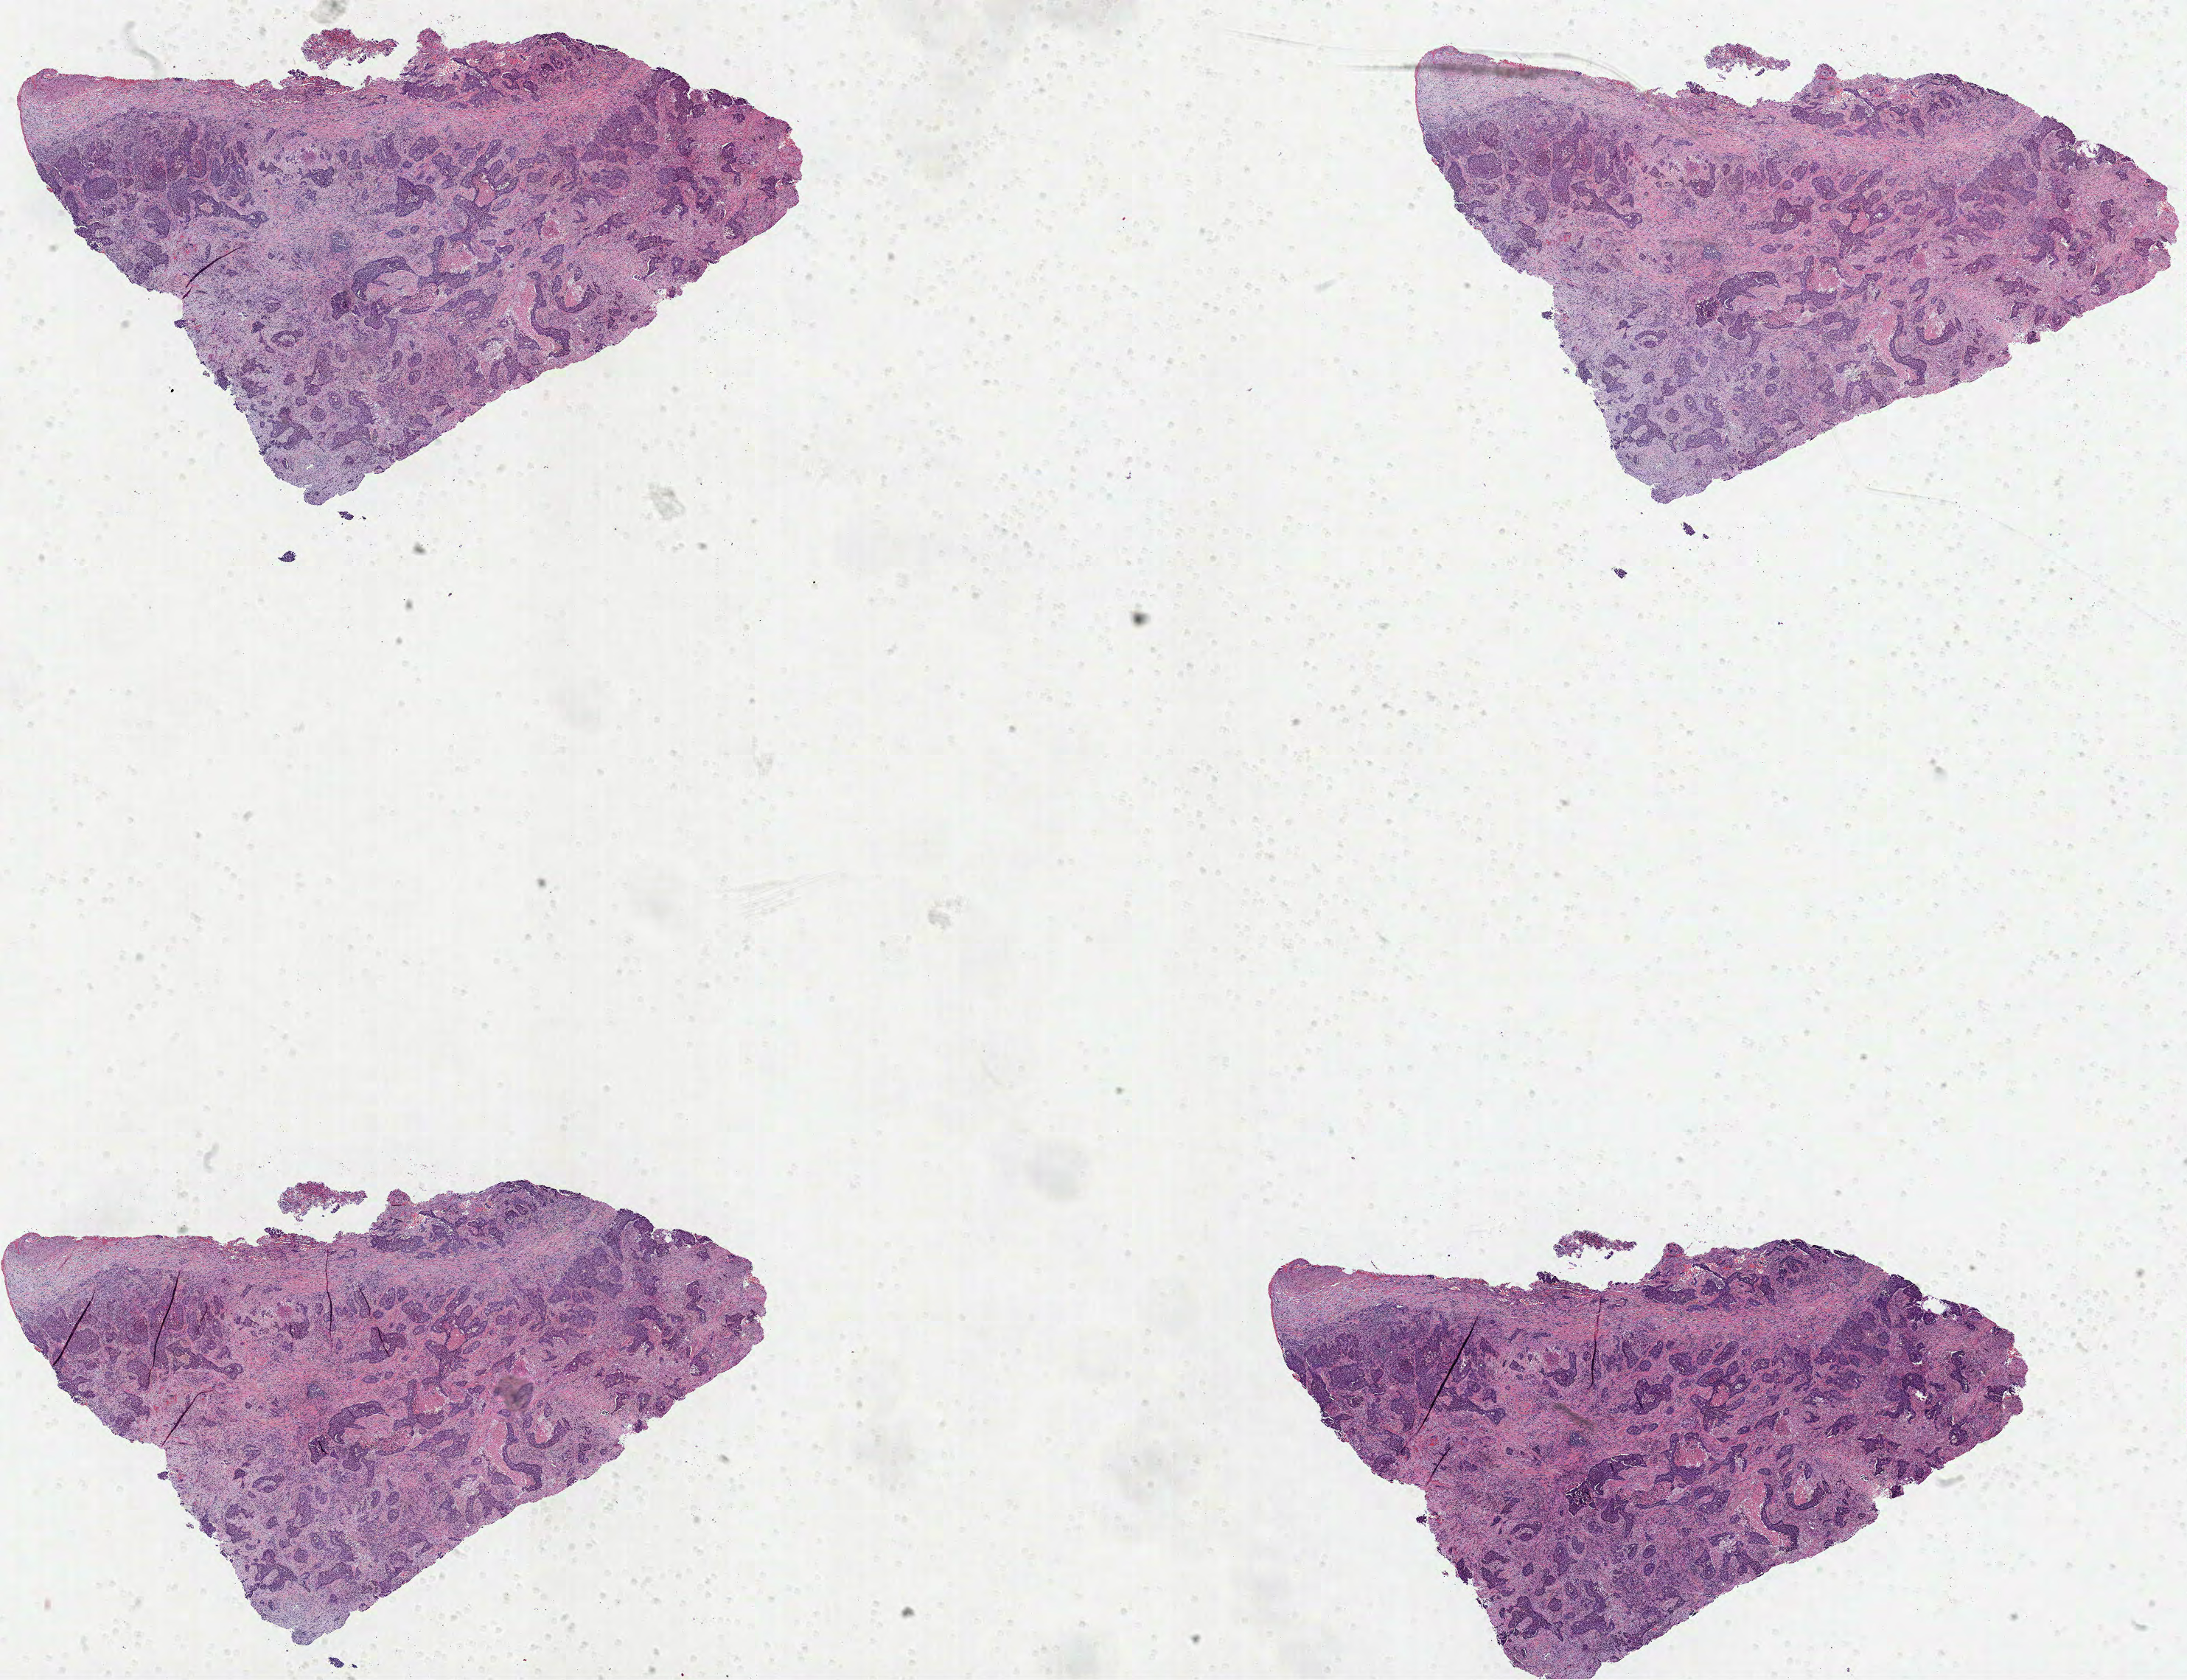
Digitized H&E-stained tissue section (whole slide), whole scanned area (about 23.9 x 18.4 mm, acquisition: 40x scan) shown as a low-resolution overview; formalin-fixed paraffin-embedded (FFPE) diagnostic section; primary tumour sample from the lung. Male, age 72 years at initial diagnosis.
AJCC pathologic stage: IB (7th edition). Diagnosis: Adenocarcinoma, NOS.